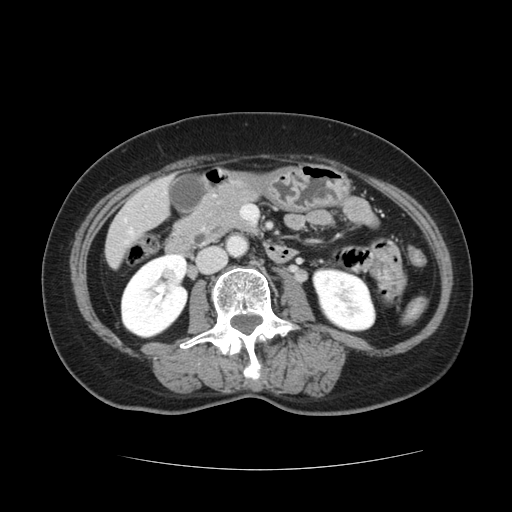
Contrast-enhanced abdominal CT, one axial slice. Position 30 of 128 along the scan axis. 120 kVp. Intravenous contrast given. Soft-tissue window (W 400 / L 40 HU). 512 × 512 image matrix. Female patient, age 67 years. Case-level facts recorded for this patient, not image findings: diagnosis: colorectal cancer liver metastases, imaged before liver resection; multiple liver metastases: yes; largest metastasis: 3 cm.
Annotated regions visible in this slice (manually delineated by an expert):
- liver: box from (x=106, y=180) to (x=169, y=265) px
- planned liver remnant (the part of the liver to remain after resection): (x=106, y=212)–(x=138, y=265)